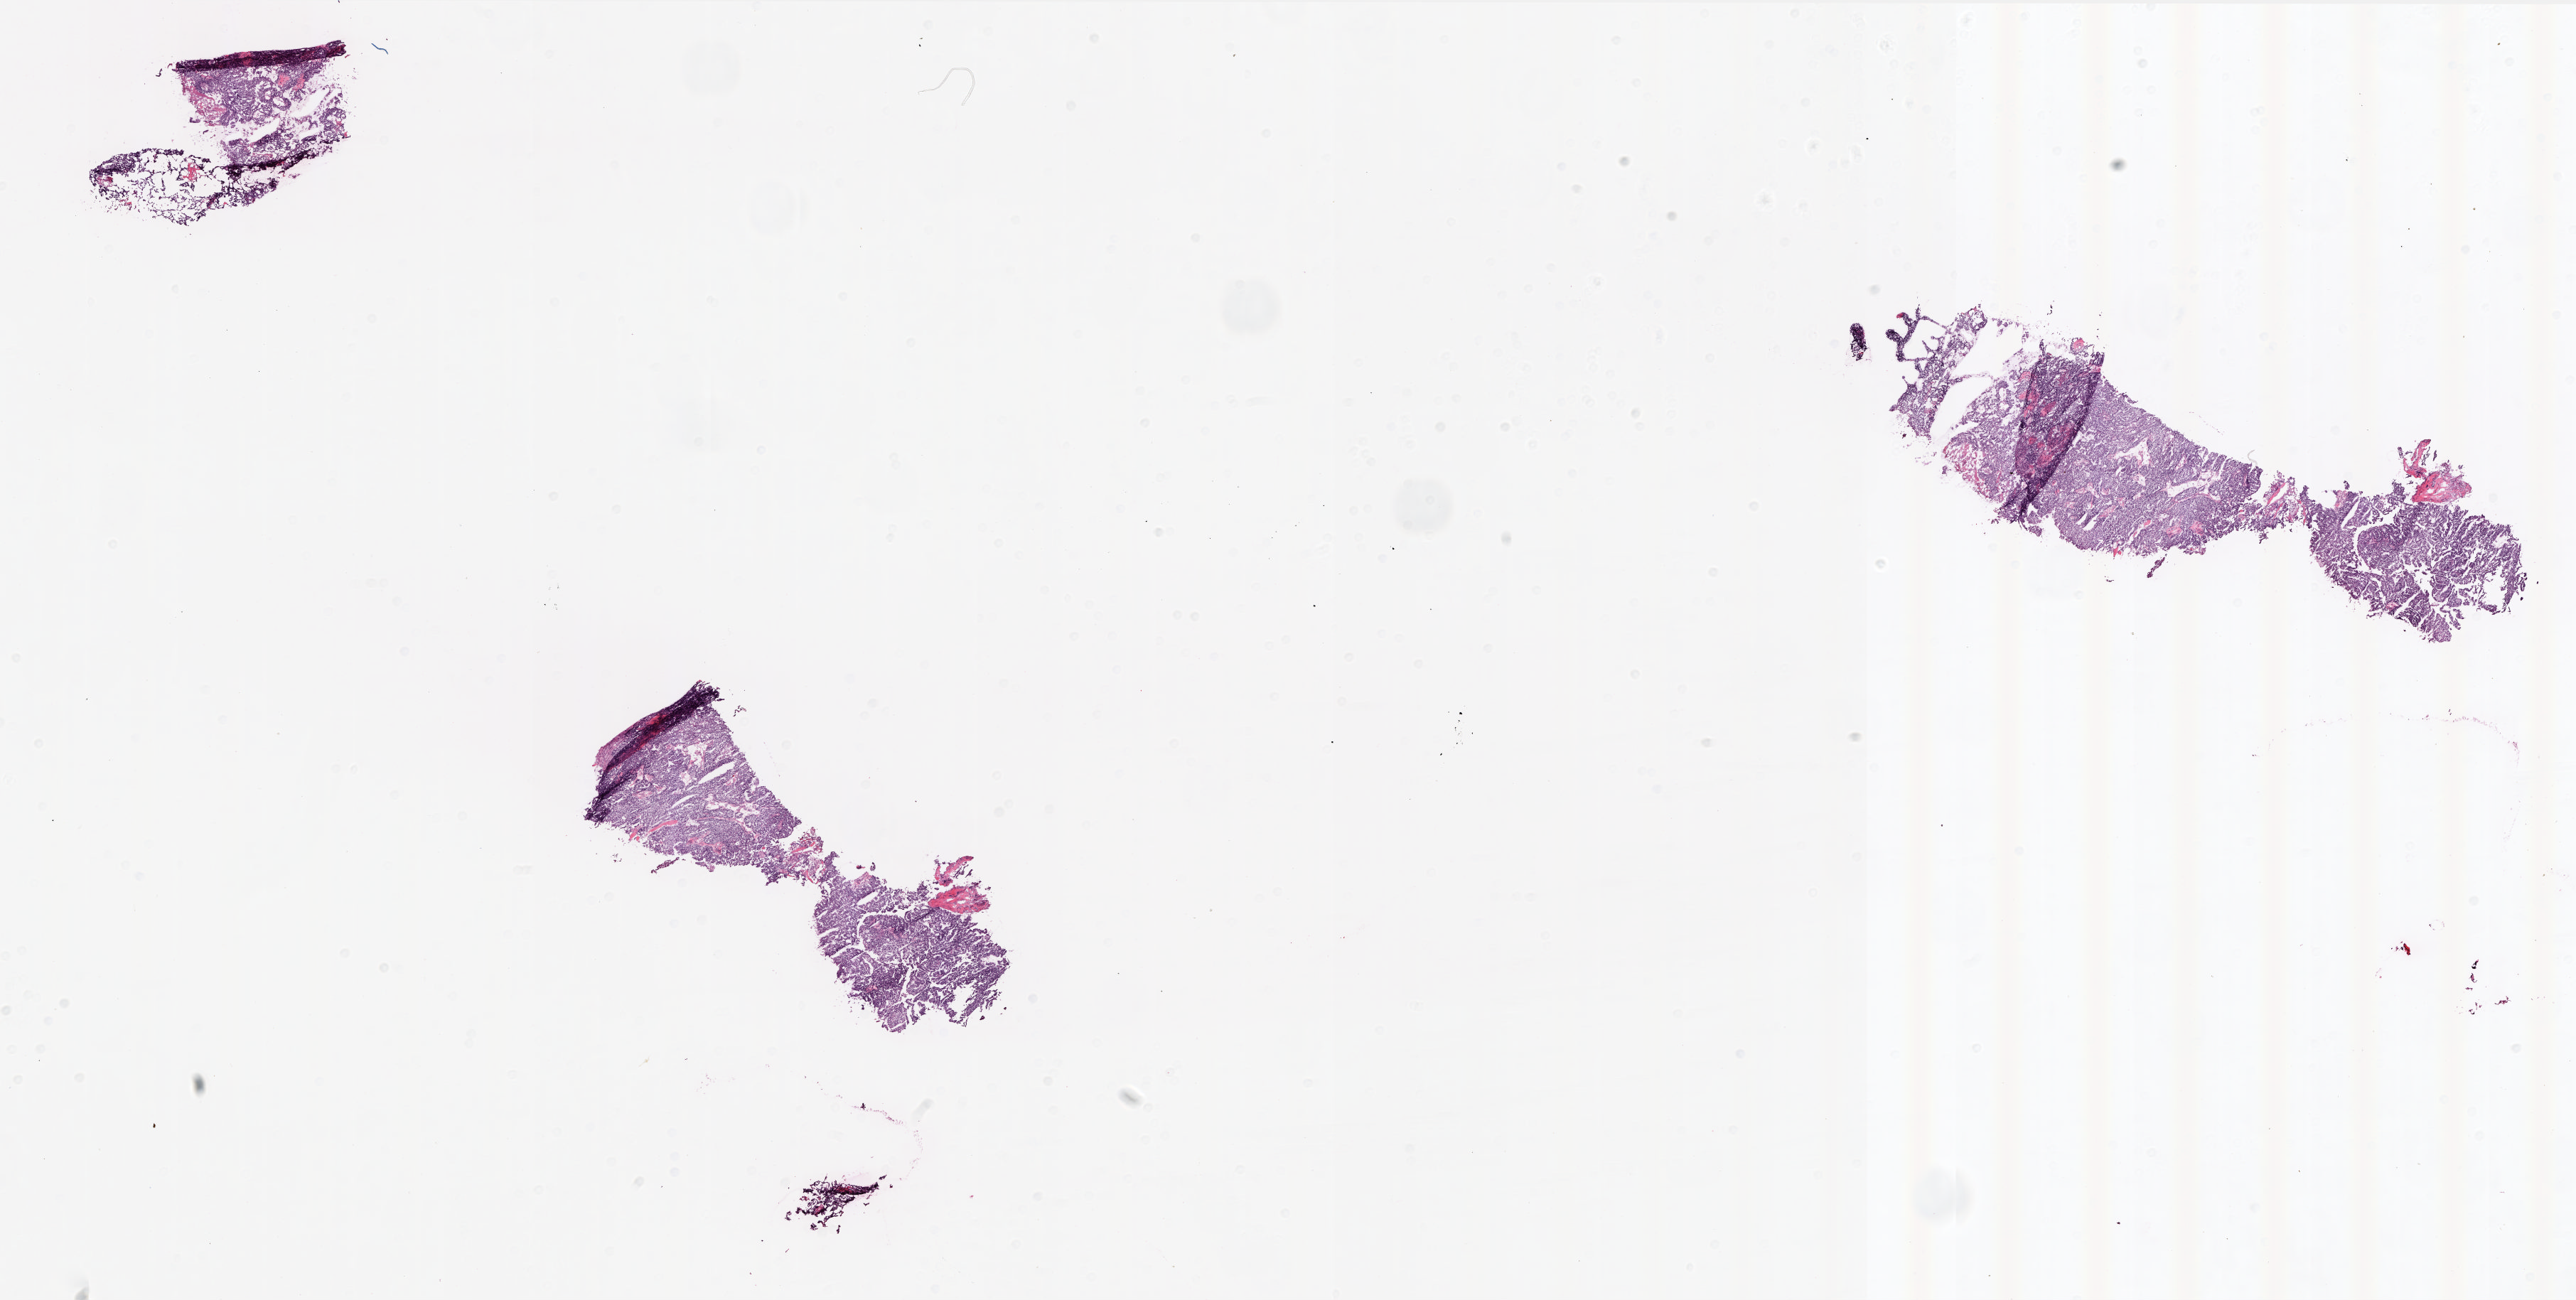
H&E whole-slide image — a low-resolution overview of the entire scanned area, about 28.9 x 14.6 mm (acquisition: 20x scan). Frozen section from the top of the tissue portion. Ovary, primary tumour sample. Female, age 57 years at initial diagnosis. Histologic grade: G3 (poorly differentiated). Slide review estimates, as recorded: tumour cells 95%, tumour nuclei 99%, normal cells 0%, stromal cells 2%, necrosis 3%.
FIGO stage: IV. Diagnosis: Serous cystadenocarcinoma, NOS.